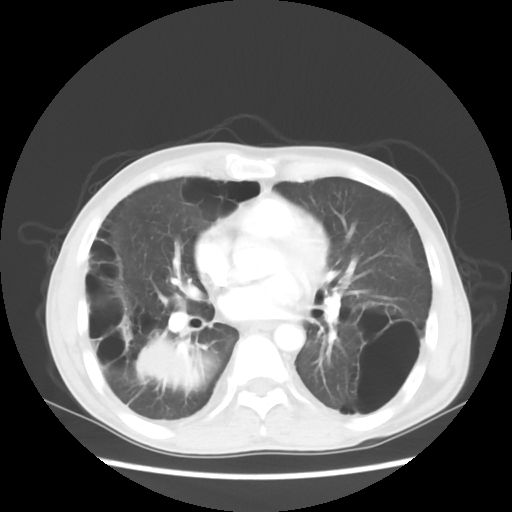
Chest CT, one axial slice. Slice 25 of 56 in the series (ordered by position). Reconstruction kernel STANDARD. 140 kVp. Lung window (W 1500 / L -600 HU). 5 mm slice thickness. 512 × 512 image matrix, field of view 351 × 351 mm. Patient: male, 41 years. Case-level facts recorded for this patient, not image findings: clinical TNM (as recorded): T4 N0 M1a; histopathological grade: G3.
Structures marked on this image (rectangle marked by the reading radiologist):
- lung tumour (recorded histology: large cell carcinoma): box from (x=108, y=318) to (x=215, y=395) px